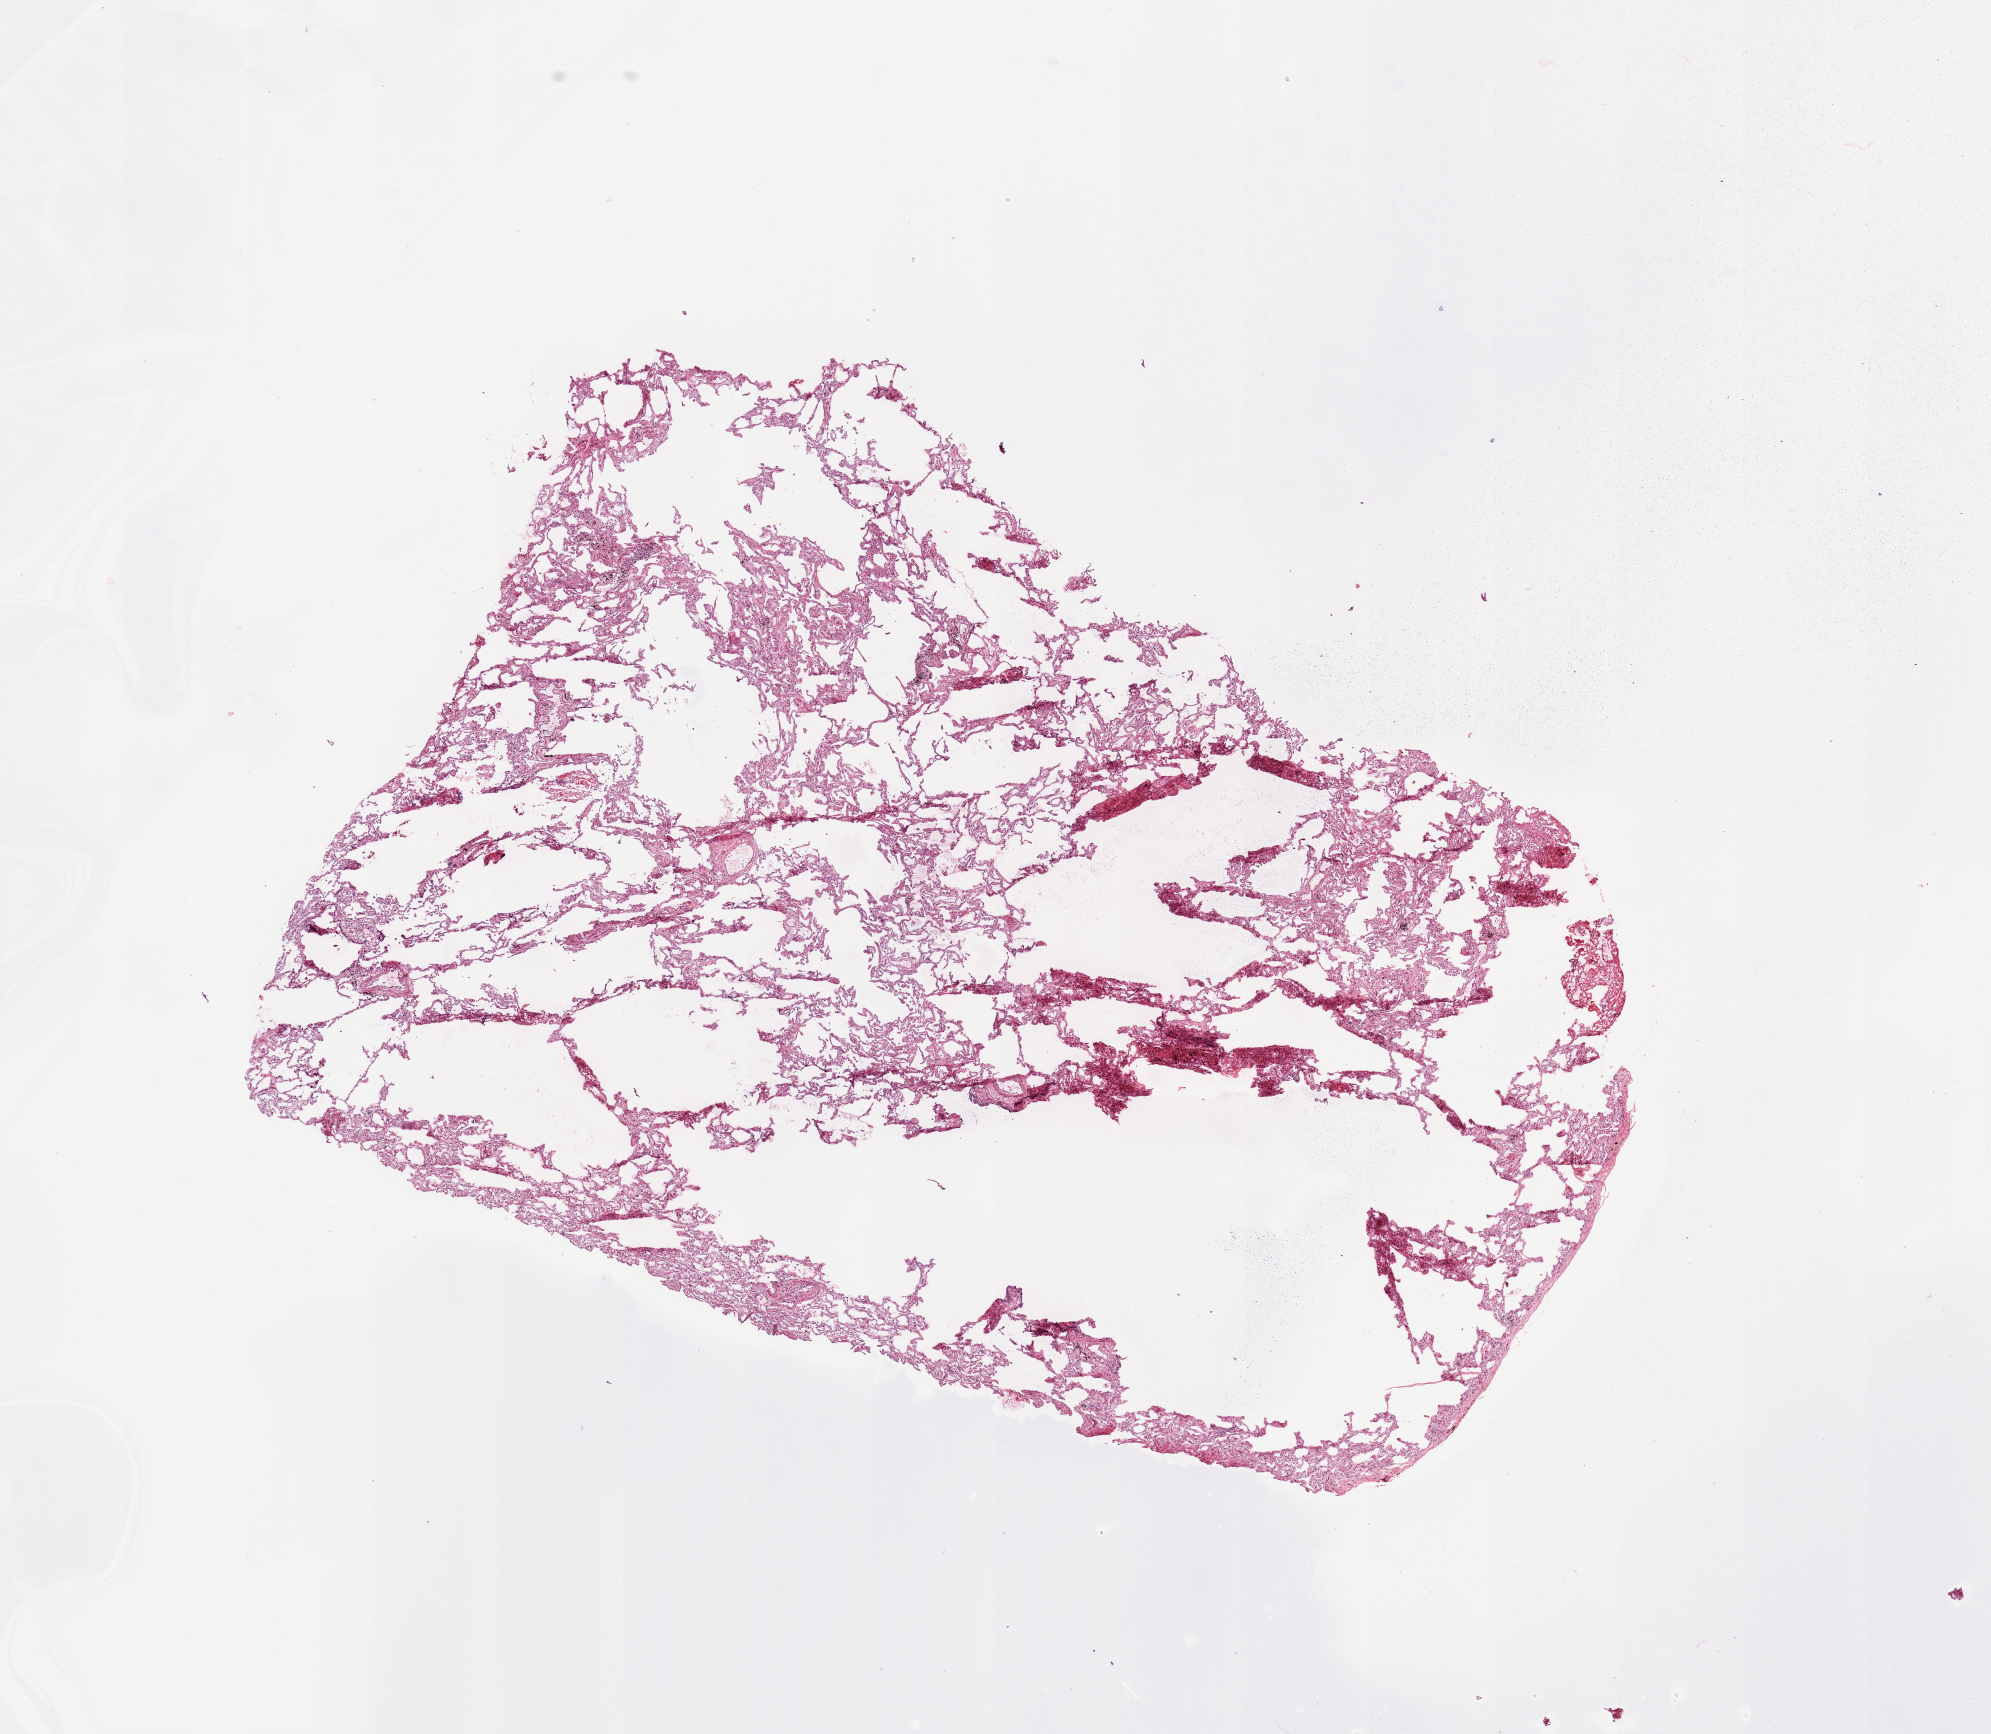
H&E whole-slide image — low-resolution overview of the scanned area, about 15.8 x 13.7 mm (acquisition: 20x scan). Lung, normal (non-tumour) tissue. Patient: female, age 75 years.
This section: normal (non-tumour) tissue from the same patient. Patient diagnosis (cohort enrolment): squamous cell carcinoma (lung).